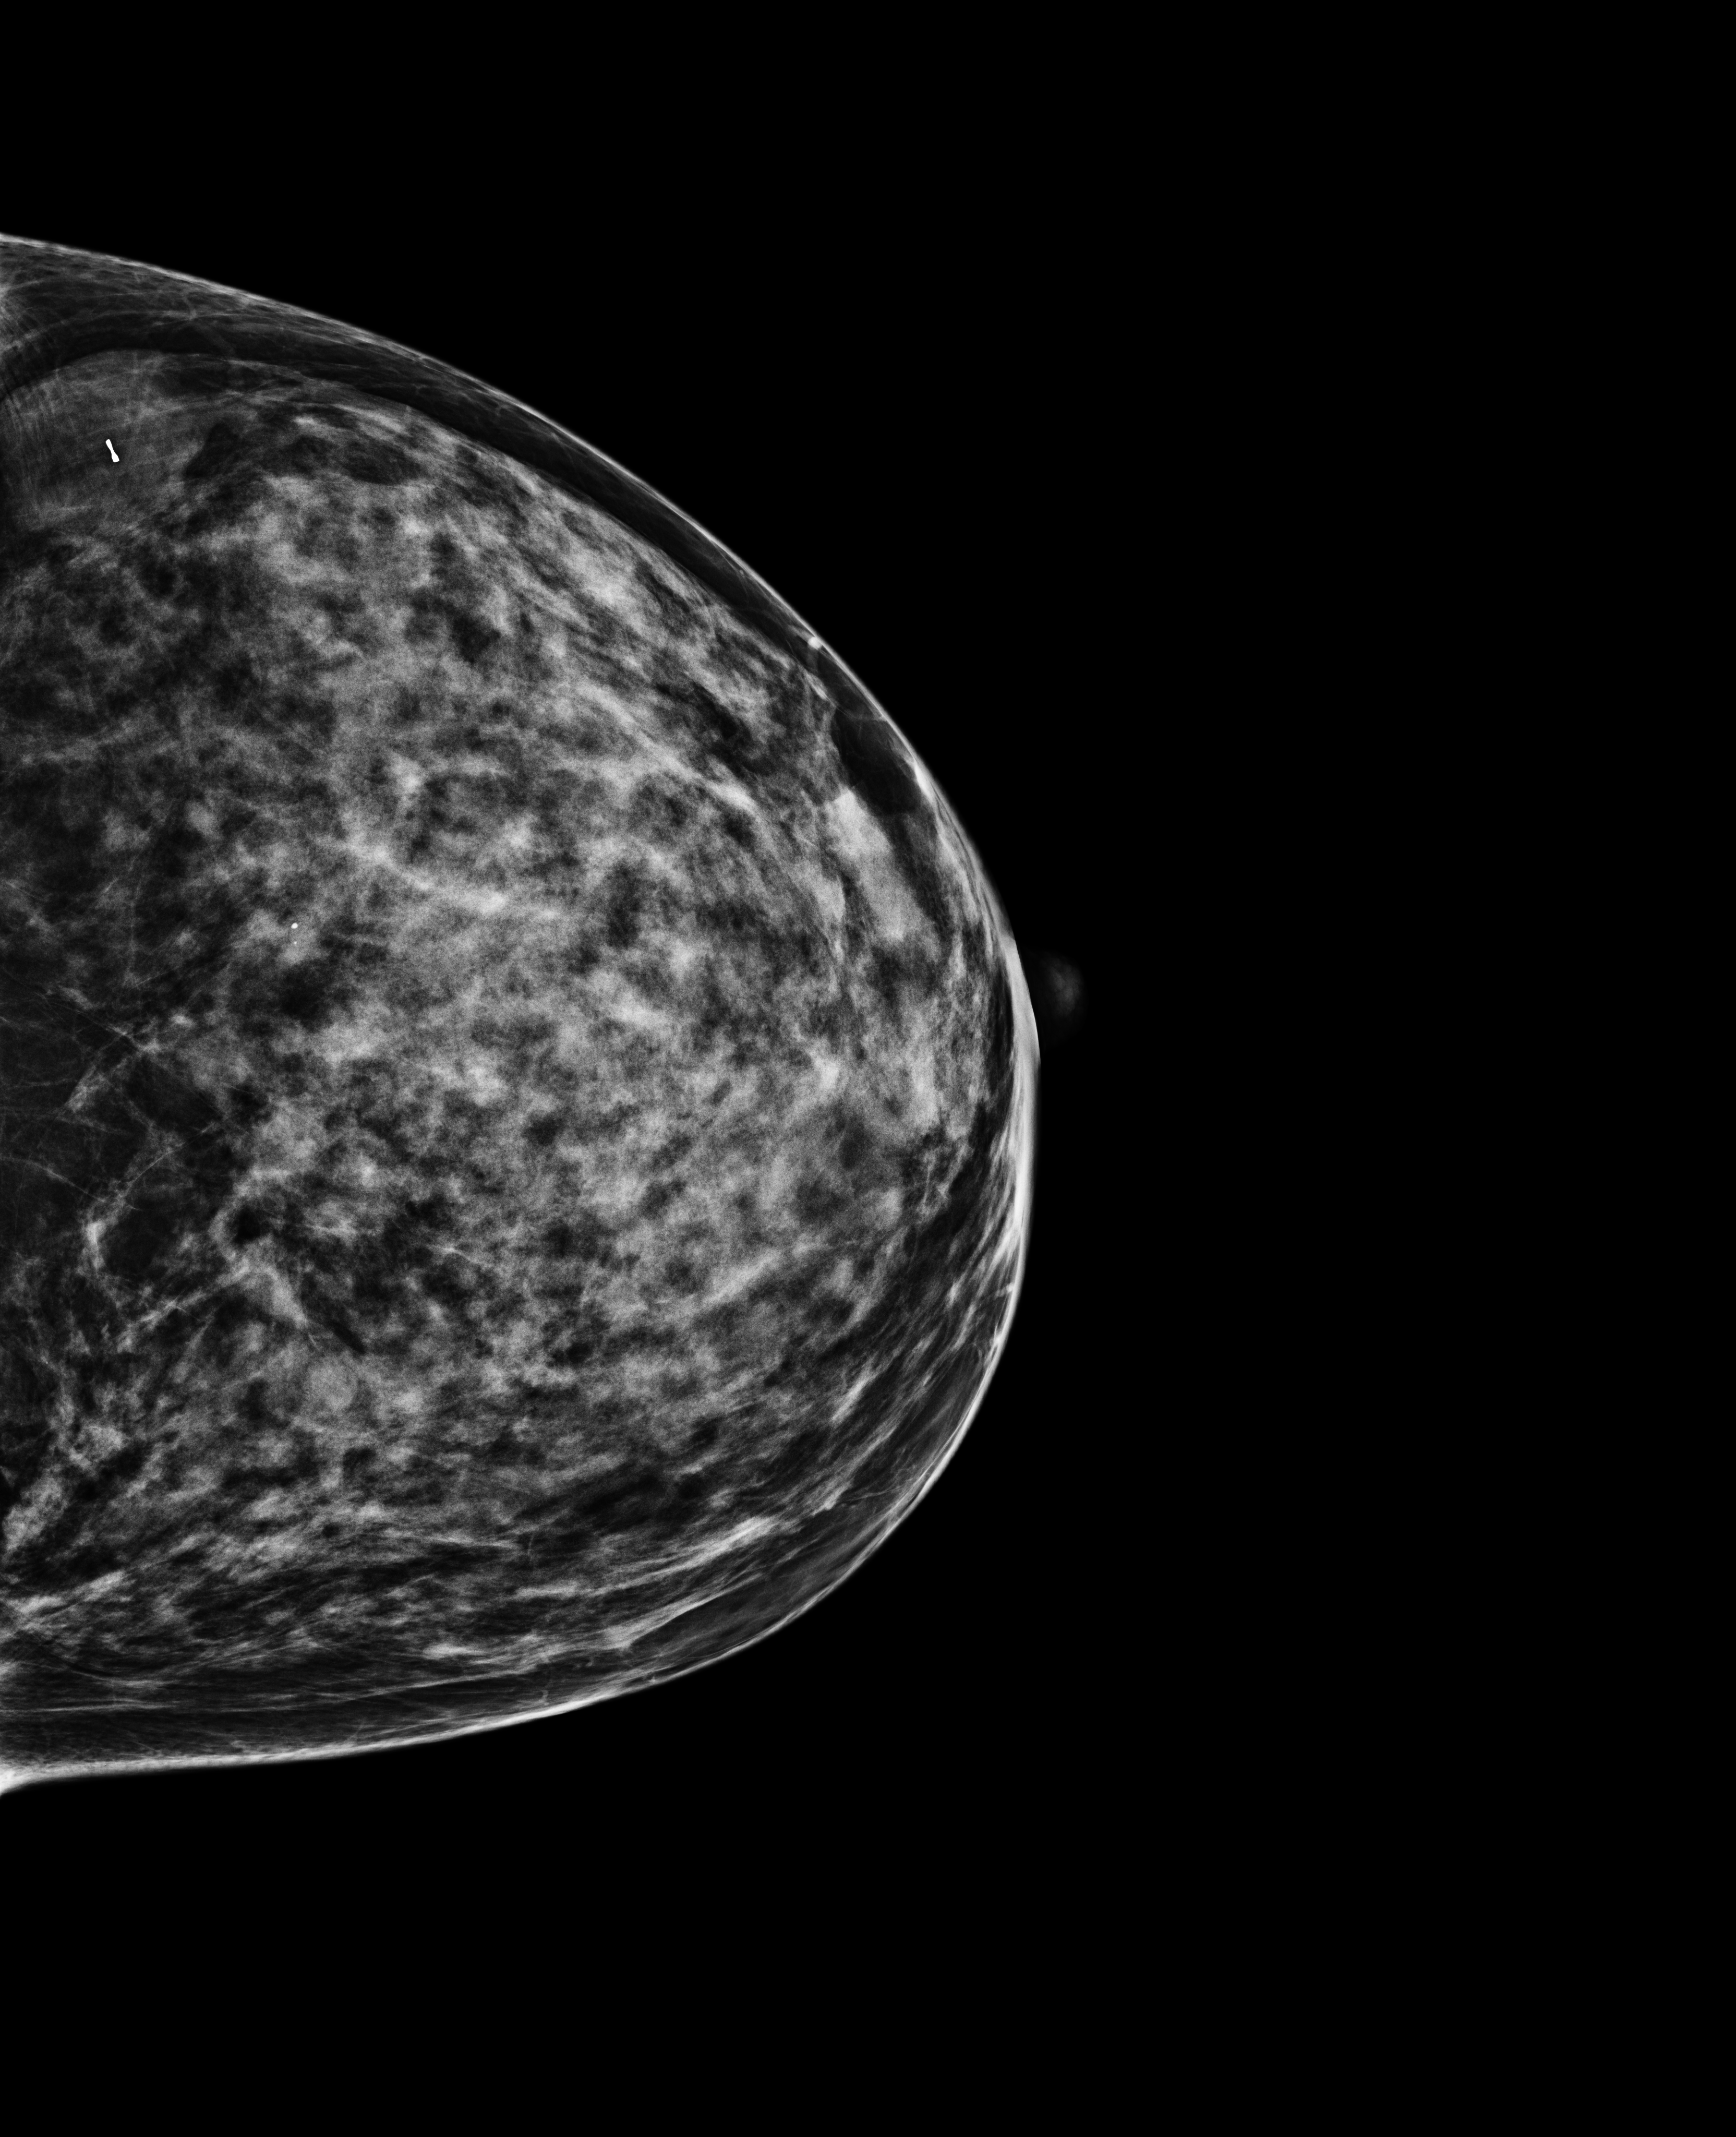
Annual screening mammography examination; compressed breast thickness 63 mm; system: Selenia Dimensions. Patient: female, 45 years.
Image type: full-field digital mammogram. Breast: left. Projection: craniocaudal (CC) view.